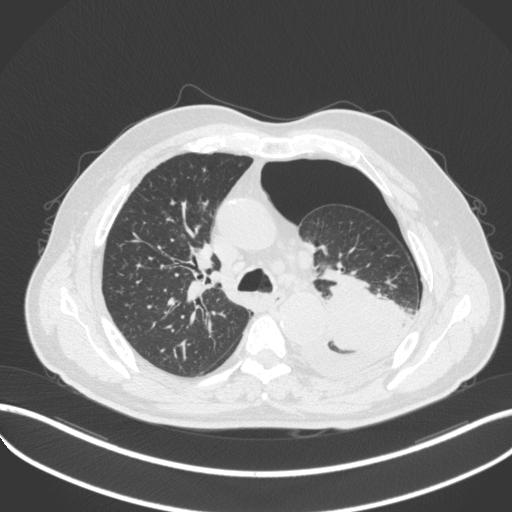
Chest CT, one axial slice; slice 345 of 466 in the series (ordered by position); reconstruction kernel B31f; lung window (W 1500 / L -600 HU); 1 mm slice thickness; 512 × 512 image matrix. Male patient, age 76 years. From the clinical record (not read from this slice): clinical TNM (as recorded): T3 N0 M1b.
Outlined on this slice (bounding box drawn by a radiologist):
- lung tumour (recorded histology: adenocarcinoma): bounding box (x1, y1, x2, y2) in pixels: (301, 267, 420, 380)